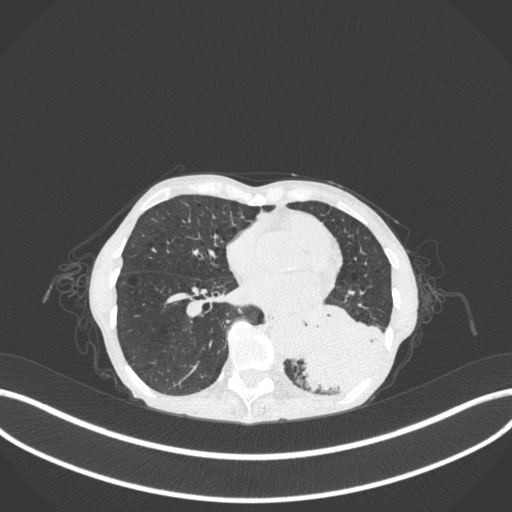
Chest CT, one axial slice. Slice 102 of 347 in the series (ordered by position). Reconstruction kernel B31f. Lung window (W 1500 / L -600 HU). 1 mm slice thickness. 512 × 512 image matrix. Patient: female, 70 years. From the clinical record (not read from this slice): clinical TNM (as recorded): T3 N0 M0.
Structures marked on this image (bounding box drawn by a radiologist):
- lung tumour (recorded histology: small cell carcinoma): bounding box <294,293,399,396> (left, top, right, bottom; pixels)